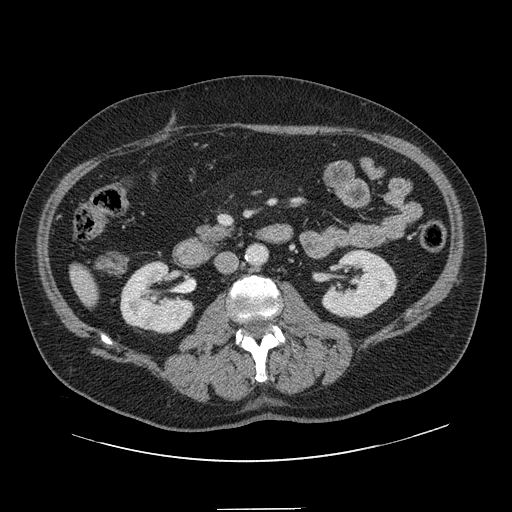
Contrast-enhanced abdominal CT, one axial slice; slice 34 of 154 in the series (ordered by position); 120 kVp; intravenous contrast given; soft-tissue window (W 400 / L 40 HU); 2.5 mm slice thickness; 512 × 512 image matrix, field of view 451 × 451 mm. Male patient, age 61 years. Case-level facts recorded for this patient, not image findings: diagnosis: colorectal cancer liver metastases, imaged before liver resection; multiple liver metastases: yes; largest metastasis: 2.6 cm; chemotherapy before resection: no.
Annotated regions visible in this slice (outlined manually by an expert reader):
- liver: bounding box [x1, y1, x2, y2] px = [72, 267, 98, 305]
- planned liver remnant (the part of the liver to remain after resection): [72, 267, 98, 306]